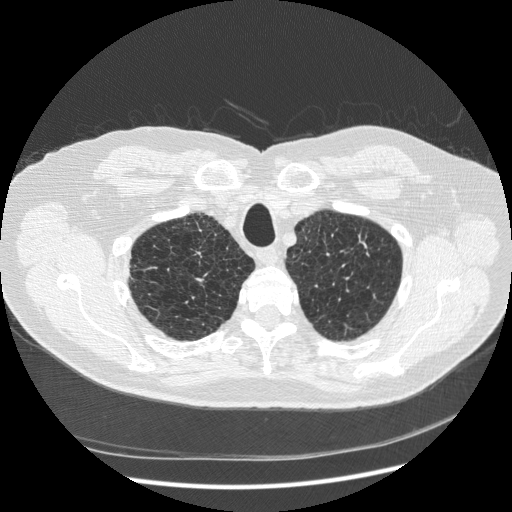
Low-dose screening chest CT, axial slice, baseline annual screen, lung window (W 1500 / L -600 HU), 1.25 mm slice thickness, standard (soft-tissue) reconstruction kernel (STANDARD). Male, age 70 years at enrolment. Former smoker at enrolment.
- Expert reader's lesion annotation, box from (x=332, y=218) to (x=387, y=273) px.
- The screening reader recorded 2 non-calcified nodules or masses ≥4 mm on this exam; which of them this box marks is not recorded.
- Participant outcome: lung cancer diagnosed 816 days after this screen (after the third annual screen) — squamous cell carcinoma, NOS, left upper lobe, moderately differentiated (G2), stage IA (AJCC 6th edition), 18 mm at pathology.